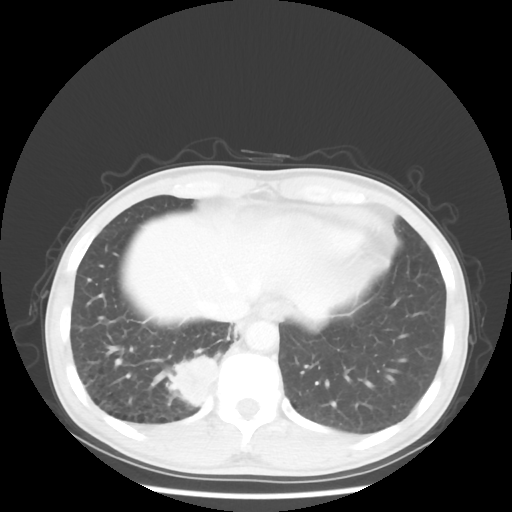
Chest CT, one axial slice. Slice 10 of 58 in the series (ordered by position). 100 kVp. Lung window (W 1500 / L -600 HU). 5 mm slice thickness. 512 × 512 image matrix. Patient: male, 56 years. From the clinical record (not read from this slice): clinical TNM (as recorded): T2 N1 M1; histopathological grade: G1.
Outlined on this slice (bounding box drawn by a radiologist):
- lung tumour (recorded histology: adenocarcinoma): bounding box [x1, y1, x2, y2] px = [170, 349, 219, 409]